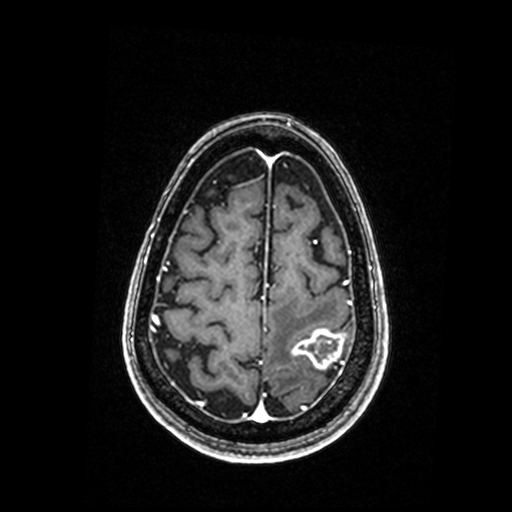
Brain MRI from a brain-tumour surgery series, one axial slice. Position 49 of 192 along the scan axis. T1-weighted post-contrast. 0.98 mm slice thickness. 512 × 512 image matrix. From the clinical record (not read from this slice): histopathology: Metastastic Carcinoma, Poorly Differentiated; tumour location: Left Parietal.
Outlined on this slice (manually delineated by an expert):
- tumour: bounding box [x1, y1, x2, y2] px = [293, 329, 344, 369]